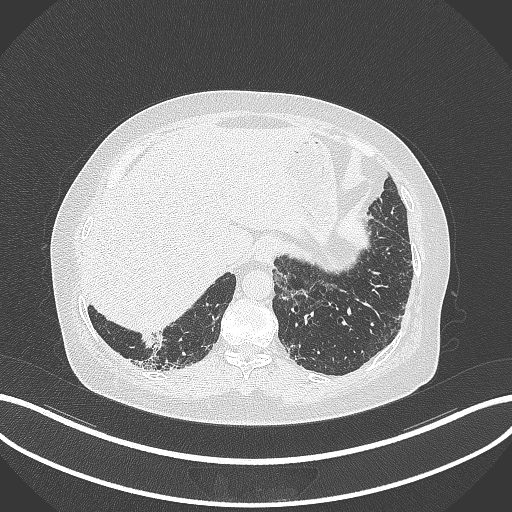
Chest CT, one axial slice; position 13 of 296 along the scan axis; lung window (W 1500 / L -600 HU); 1 mm slice thickness; 512 × 512 image matrix, field of view 400 × 400 mm. Patient: female, 65 years. From the clinical record (not read from this slice): clinical TNM (as recorded): T2b N1 M0.
Annotated regions visible in this slice (rectangle marked by the reading radiologist):
- lung tumour (recorded histology: adenocarcinoma): bounding box [x1, y1, x2, y2] px = [137, 332, 172, 356]